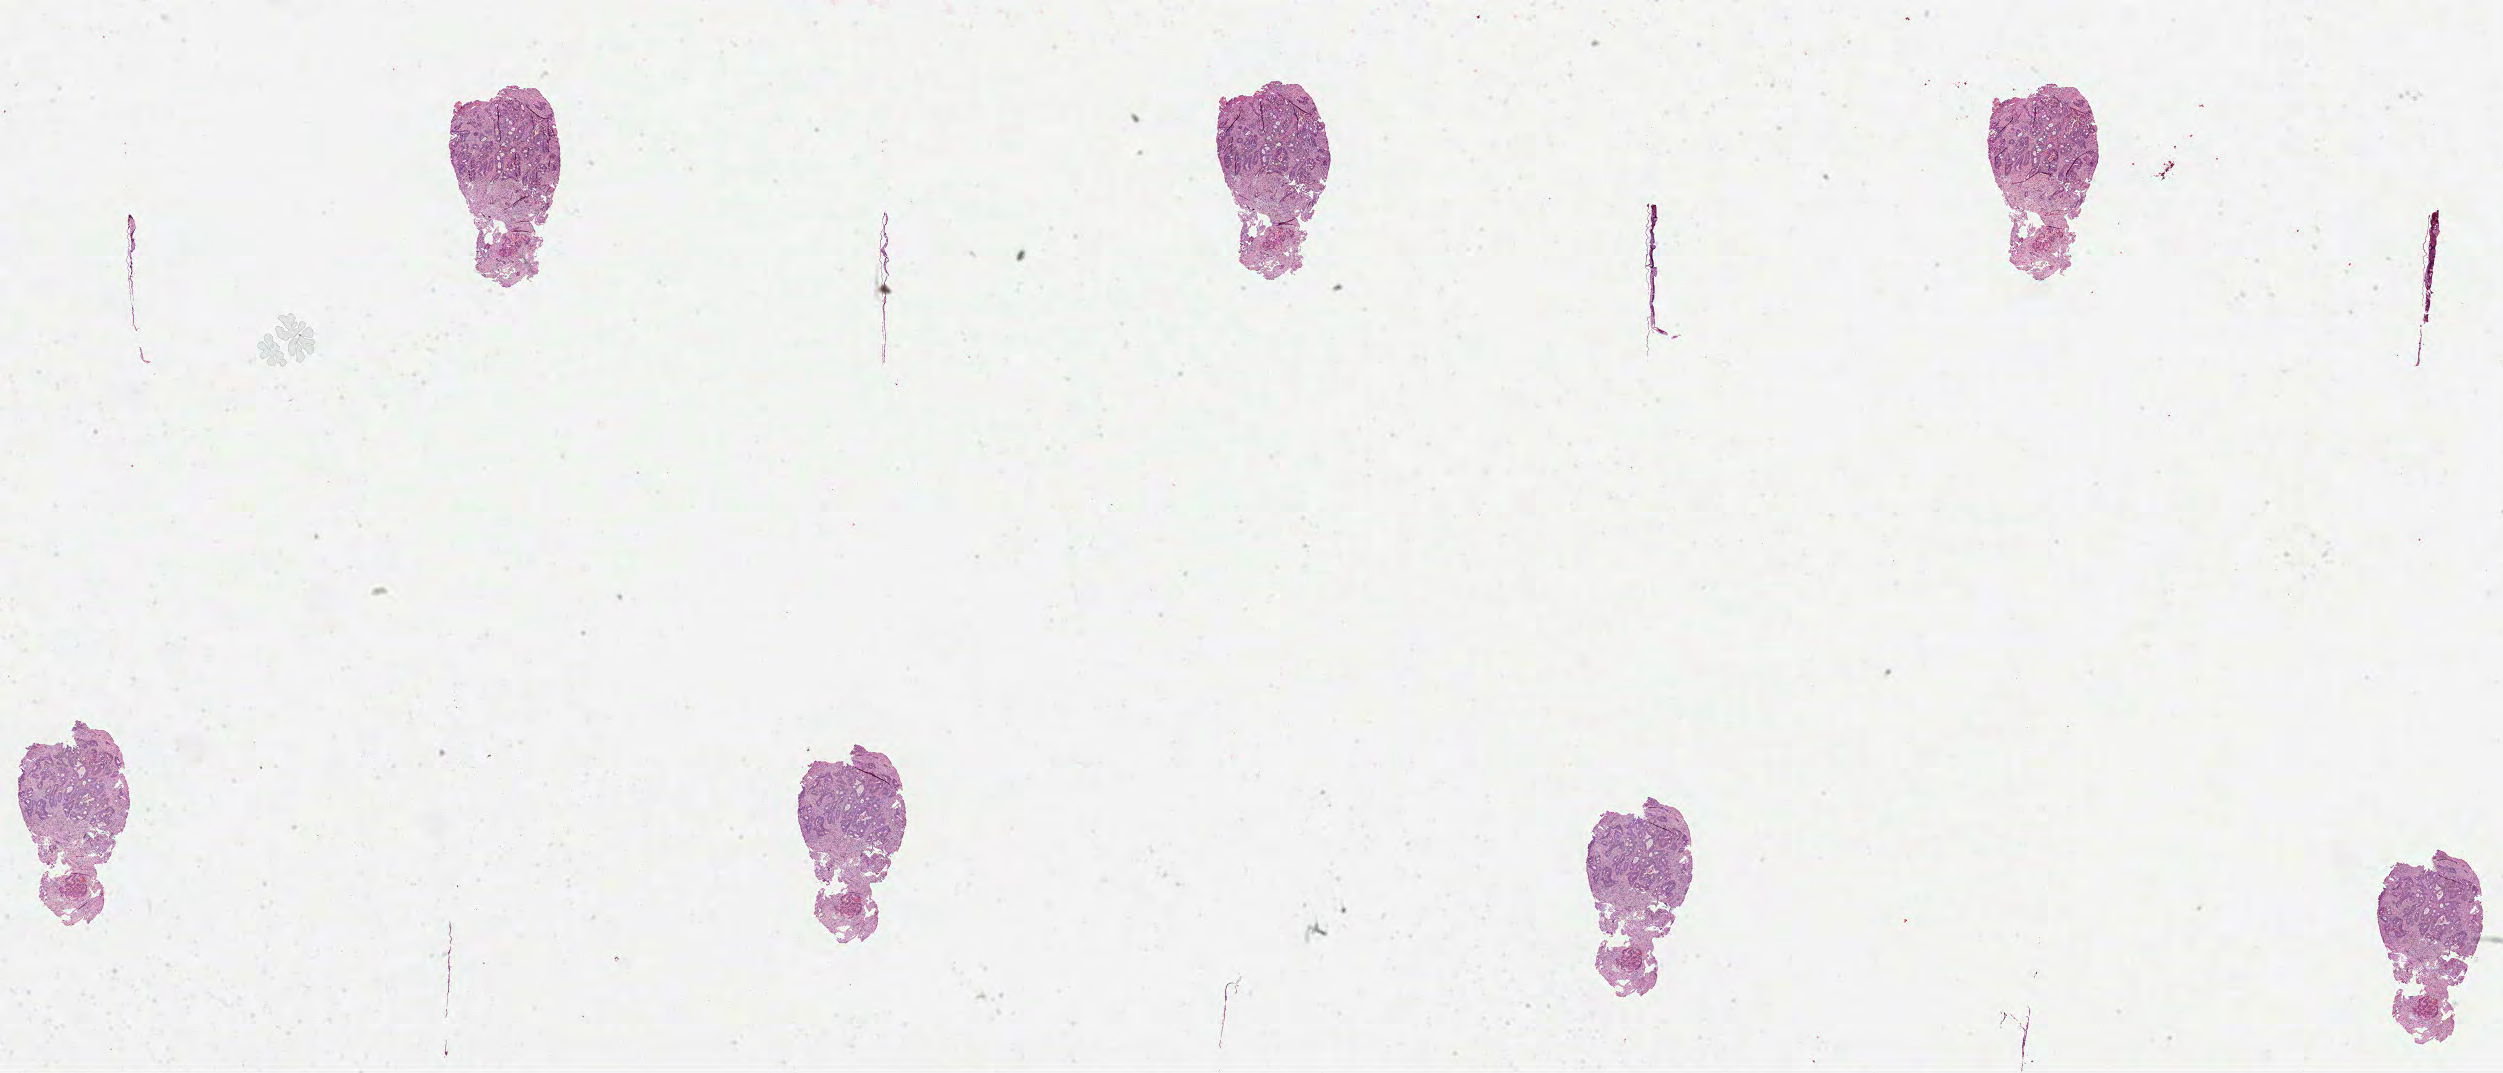
Whole-slide histology image, H&E-stained — low-resolution overview of the scanned area, about 40.4 x 17.3 mm (acquisition: 40x scan); formalin-fixed paraffin-embedded (FFPE) diagnostic section; primary tumour sample from the rectum. Patient: male, age at initial diagnosis 74 years.
Diagnosis: Adenocarcinoma, NOS.